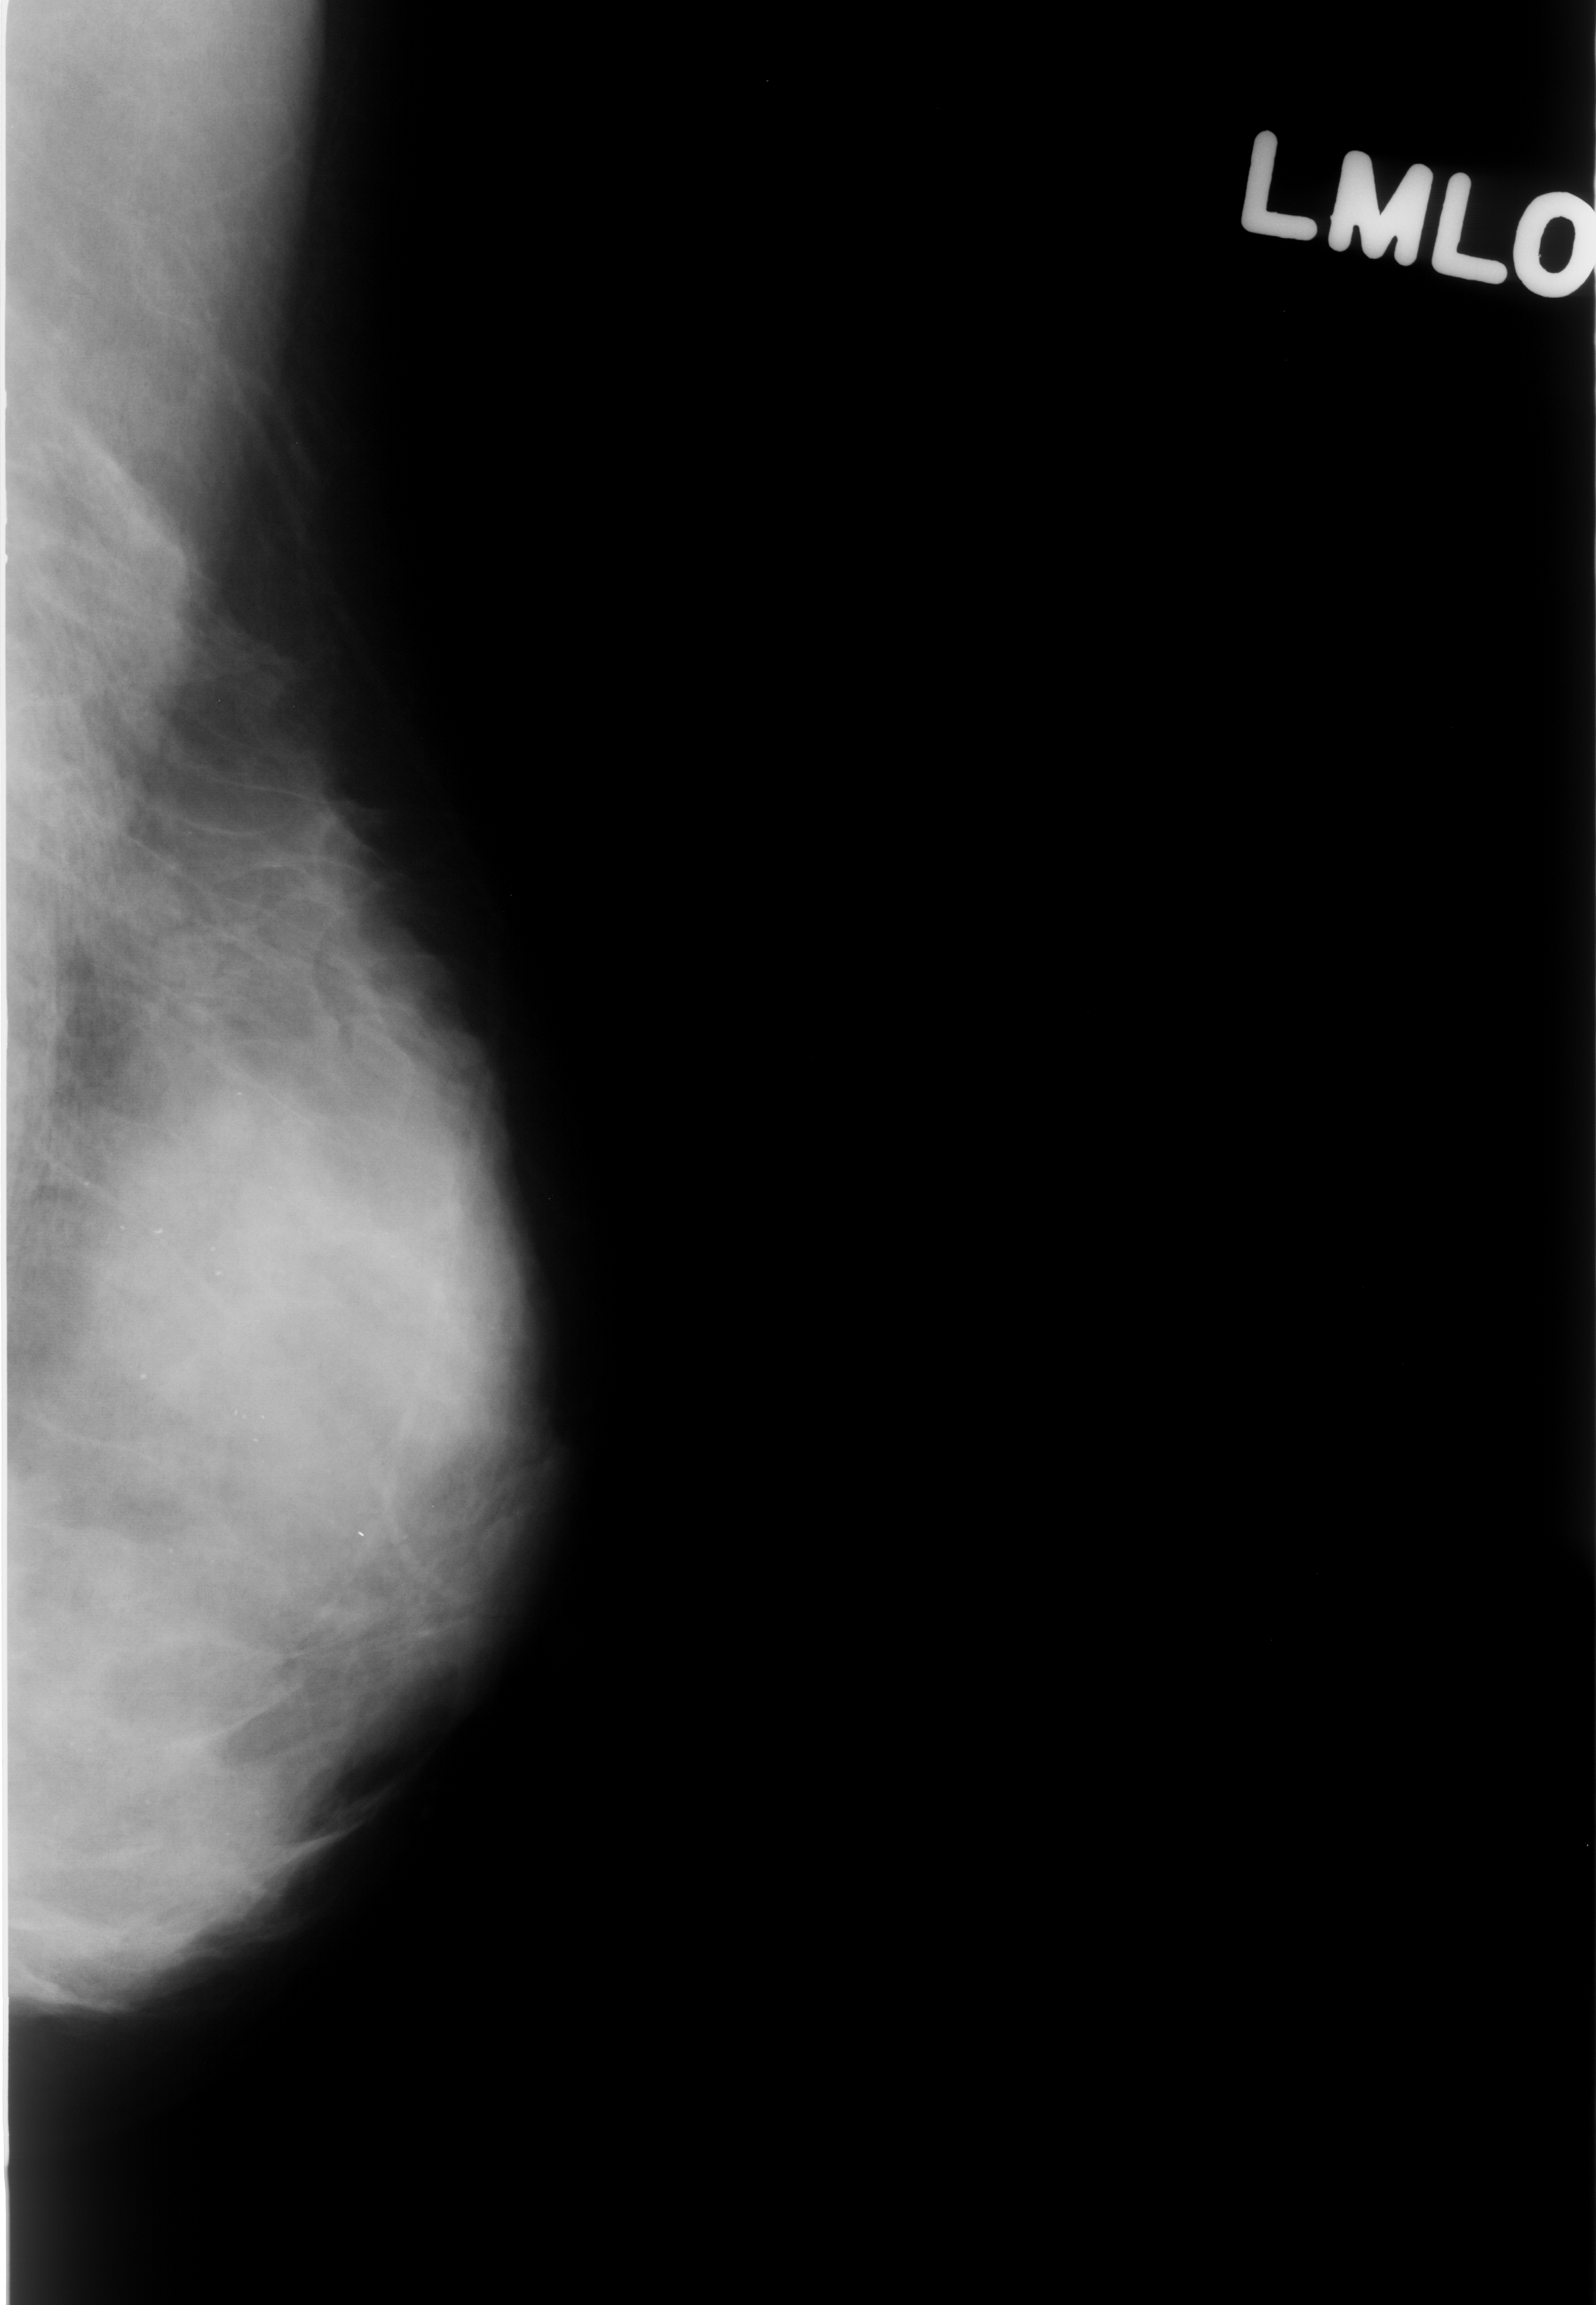
Digitized screen-film mammogram. Left breast. MLO view. BI-RADS breast density category 4 (scale 1–4). 1596 × 2305 image matrix.
Marked abnormalities (boxes around the expert regions of interest):
- calcifications, morphology punctate, distribution diffusely scattered; BI-RADS assessment category 2; subtlety rating 4 on a 1 (subtle) to 5 (obvious) scale; pathology result (as recorded, not read from the image): benign: bounding box [x1, y1, x2, y2] px = [0, 1019, 569, 1930]